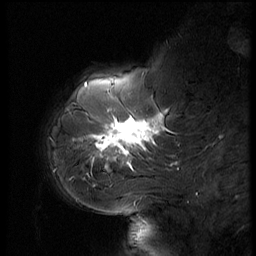
Breast MRI (dynamic contrast-enhanced), one sagittal slice. Position 15 of 56 along the scan axis. Dynamic contrast-enhanced series, image 2 of 3 at this slice position (ordered by acquisition). 1.5 T. TE 4.2 ms, TR 9 ms. 256 × 256 image matrix, field of view 180 × 180 mm. Patient: female, 61 years. From the clinical record (not read from this slice): setting: breast cancer imaged before/during neoadjuvant chemotherapy; receptor status: HR-positive, HER2-negative.
Outlined on this slice (semi-automatically segmented with operator editing):
- analysis volume of interest (the breast-tissue region the enhancement analysis was run in; not a lesion): bounding box (x1, y1, x2, y2) in pixels: (65, 74, 185, 175)
- tumour enhancement mask (voxels above the 140 % enhancement threshold inside the analysis volume of interest): (93, 113, 163, 169)